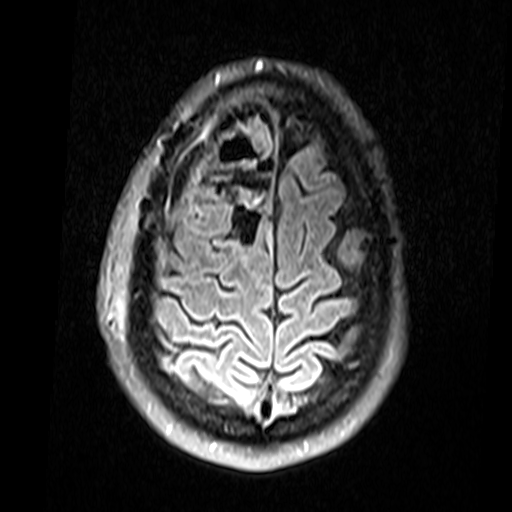
Brain MRI from a brain-tumour surgery series, one axial slice; slice 52 of 74 in the series (ordered by position); T2 FLAIR; 512 × 512 image matrix, field of view 220 × 220 mm. From the clinical record (not read from this slice): histopathology: Glial fibroma; tumour location: Right Frontal.
Annotated regions visible in this slice (outlined manually by an expert reader):
- residual tumour: box from (x=231, y=189) to (x=263, y=250) px